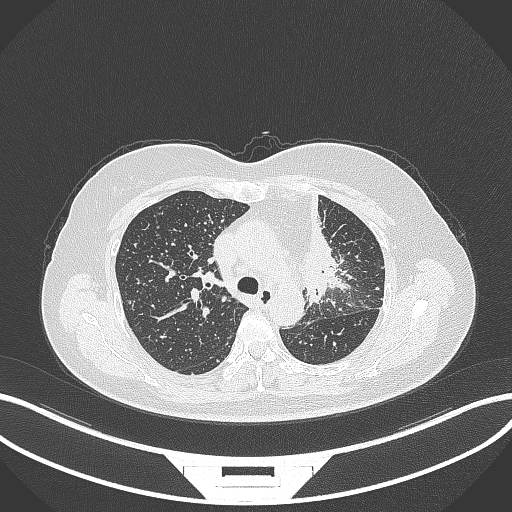
Chest CT, one axial slice. Position 230 of 348 along the scan axis. Reconstruction kernel B70f. 120 kVp. Lung window (W 1500 / L -600 HU). 512 × 512 image matrix, field of view 400 × 400 mm. Patient: female, 49 years. Case-level facts recorded for this patient, not image findings: clinical TNM (as recorded): T1c N0 M1.
Annotated regions visible in this slice (rectangle marked by the reading radiologist):
- lung tumour (recorded histology: adenocarcinoma): bounding box (x1, y1, x2, y2) in pixels: (290, 186, 355, 309)